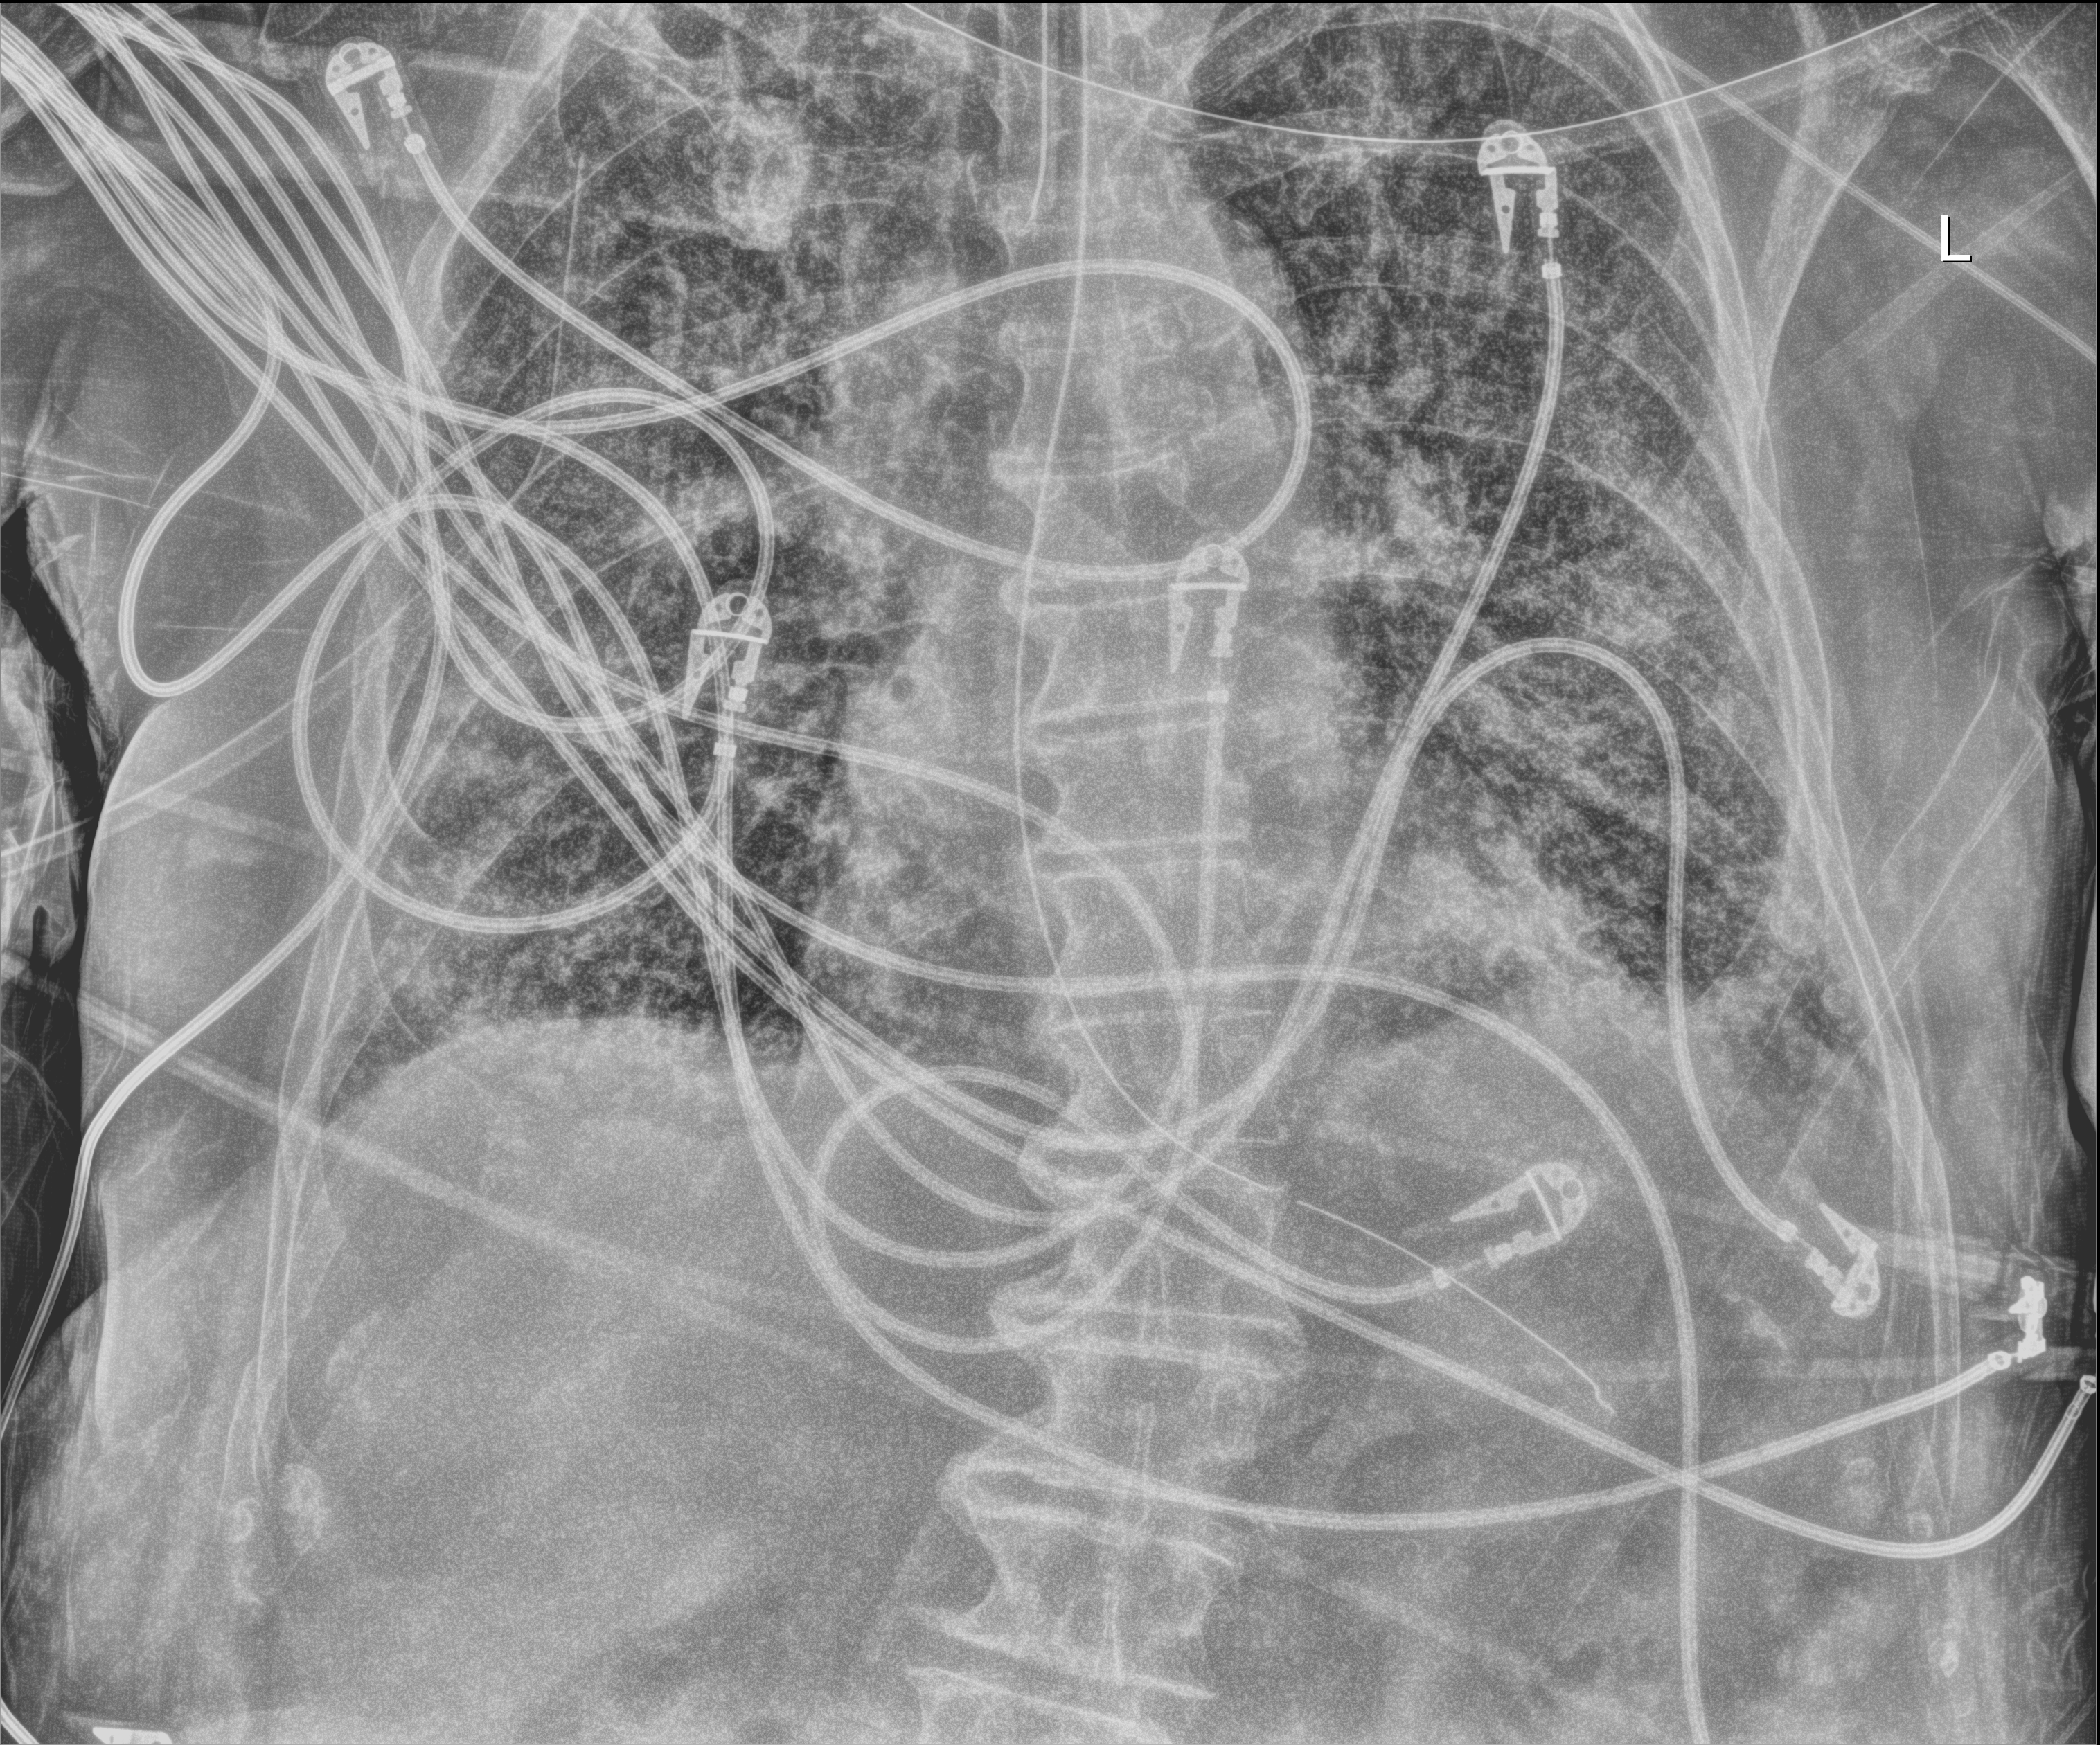
Portable chest radiograph; anteroposterior (AP) projection. Patient hospitalised with COVID-19; male, aged 75–90 years.
Admission-level facts for this patient (not findings on this image; timing relative to this image not recorded):
- mechanically ventilated during this hospital stay: yes